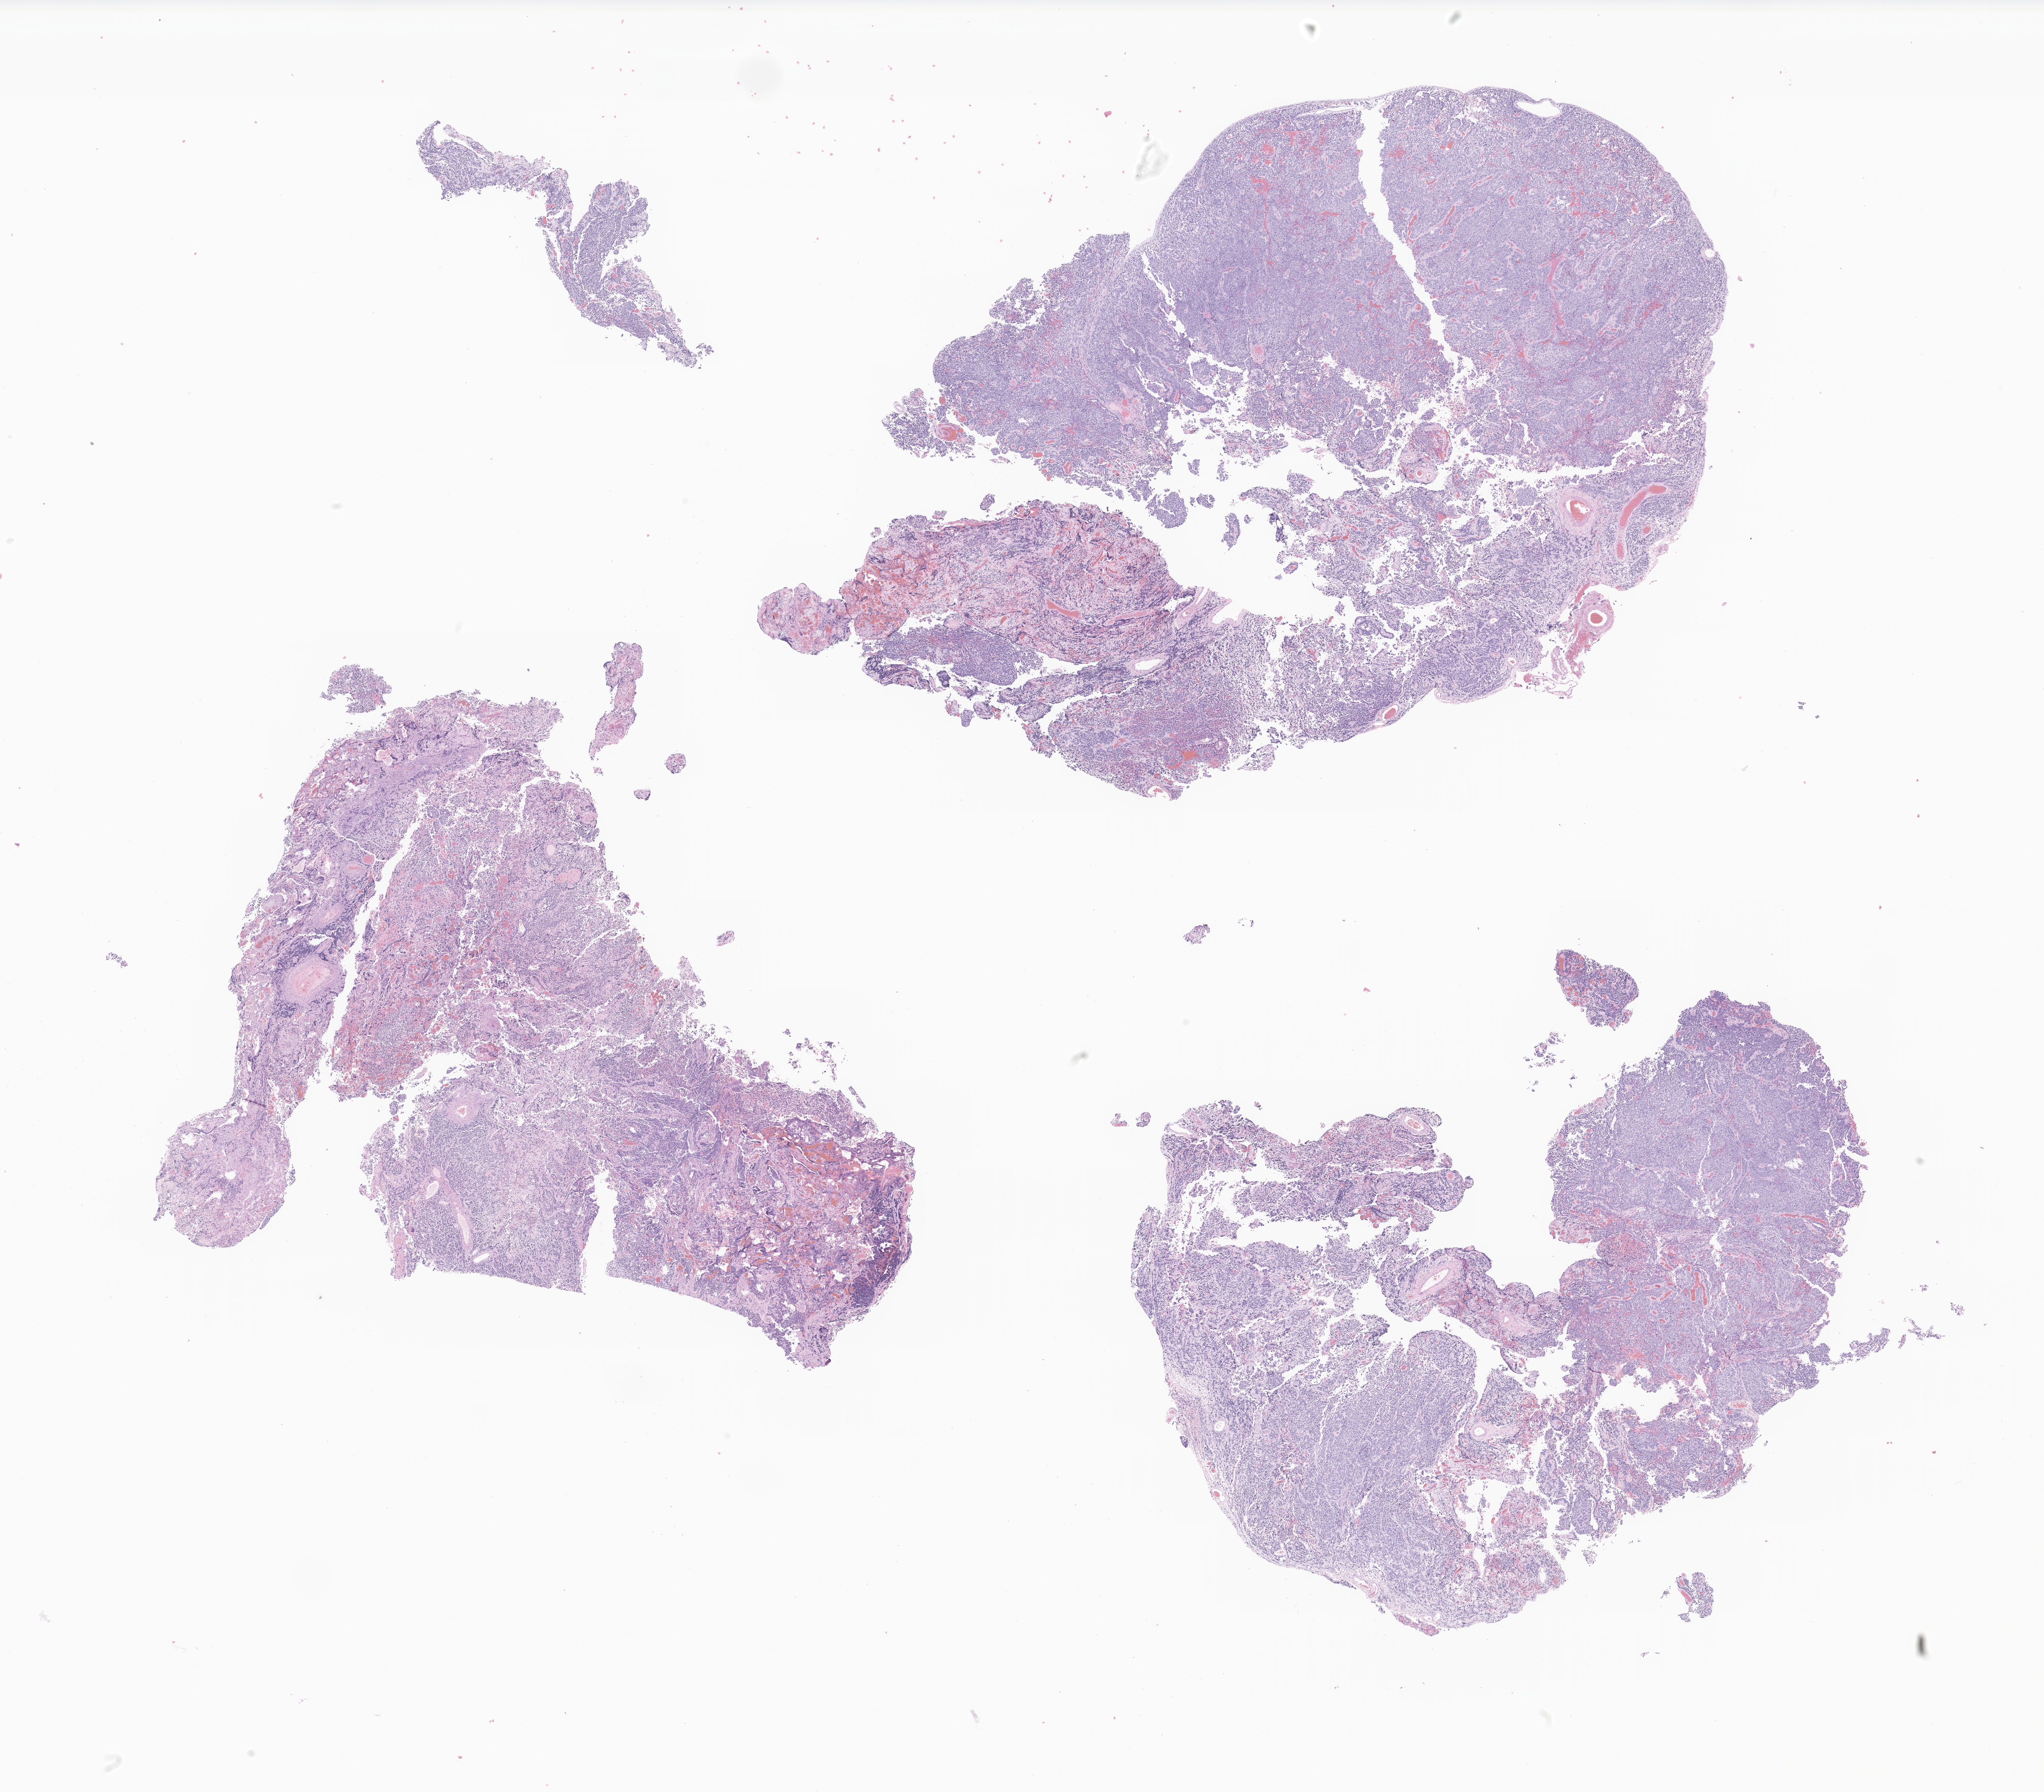
Whole-slide image, haematoxylin and eosin stain of tumor tissue from the brain — low-resolution overview of the scanned area, about 24.5 x 21.4 mm. Formalin-fixed paraffin-embedded section. Male patient, age 115 months.
Recorded diagnosis: Medulloblastoma, NOS.